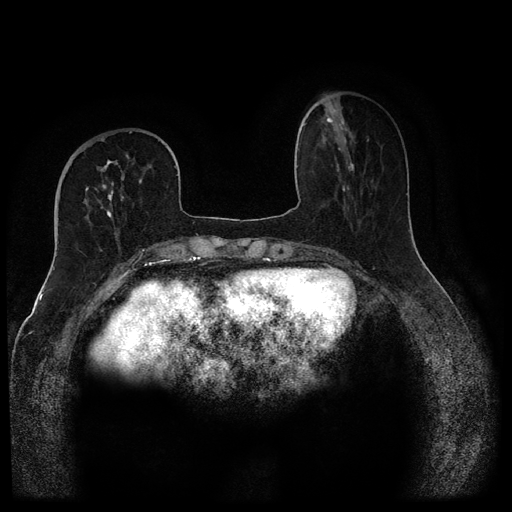
Breast MRI (dynamic contrast-enhanced, multi-phase), one axial slice; dynamic contrast-enhanced series, time point 2 of 5 at this slice position (early post-contrast); 1.5 T; TE 2.6 ms, TR 5.4 ms; 2 mm slice thickness; 512 × 512 image matrix, field of view 340 × 340 mm. Female patient, age 68 years.
Annotated regions visible in this slice (semi-automatically segmented with operator editing):
- breast lesion (labelled benign in the annotation): bounding box <322,107,351,138> (left, top, right, bottom; pixels)